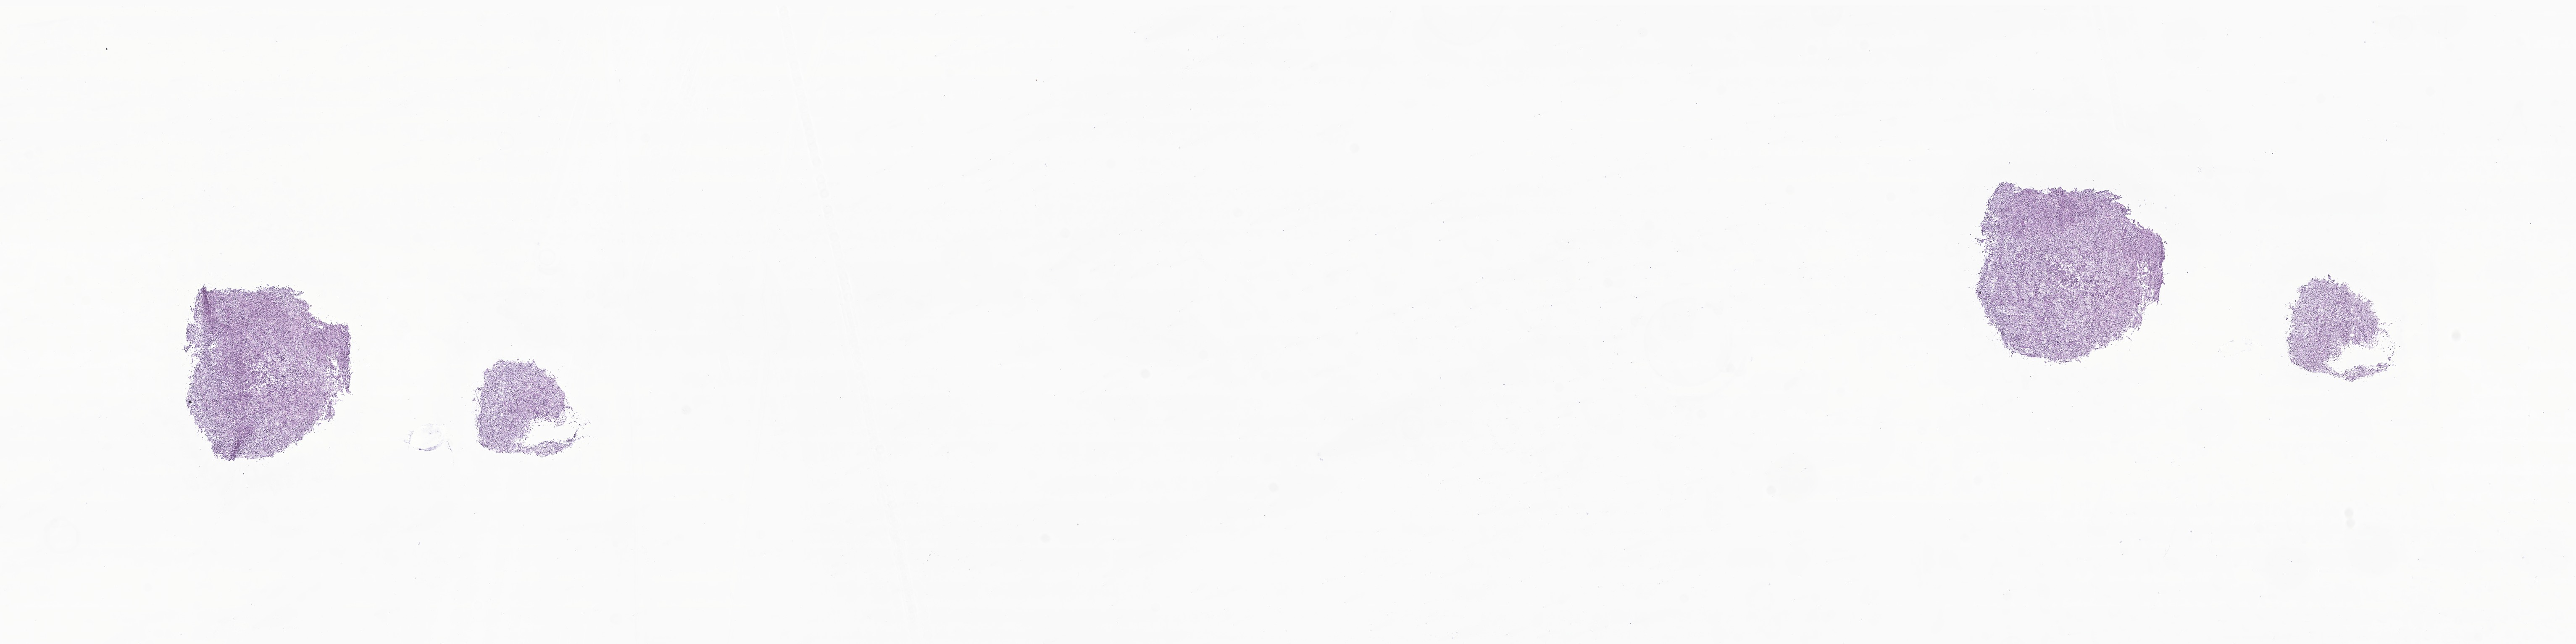
Whole-slide image, hematoxylin and eosin (H&E) stain of tumor tissue from the brain — whole scanned area (about 25.8 x 6.5 mm) shown as a low-resolution overview, cryosection (OCT / tissue freezing medium). Male patient, age 130 months (10 years 10 months).
Diagnosis (ICD-O-3 morphology term): Glioma, malignant.